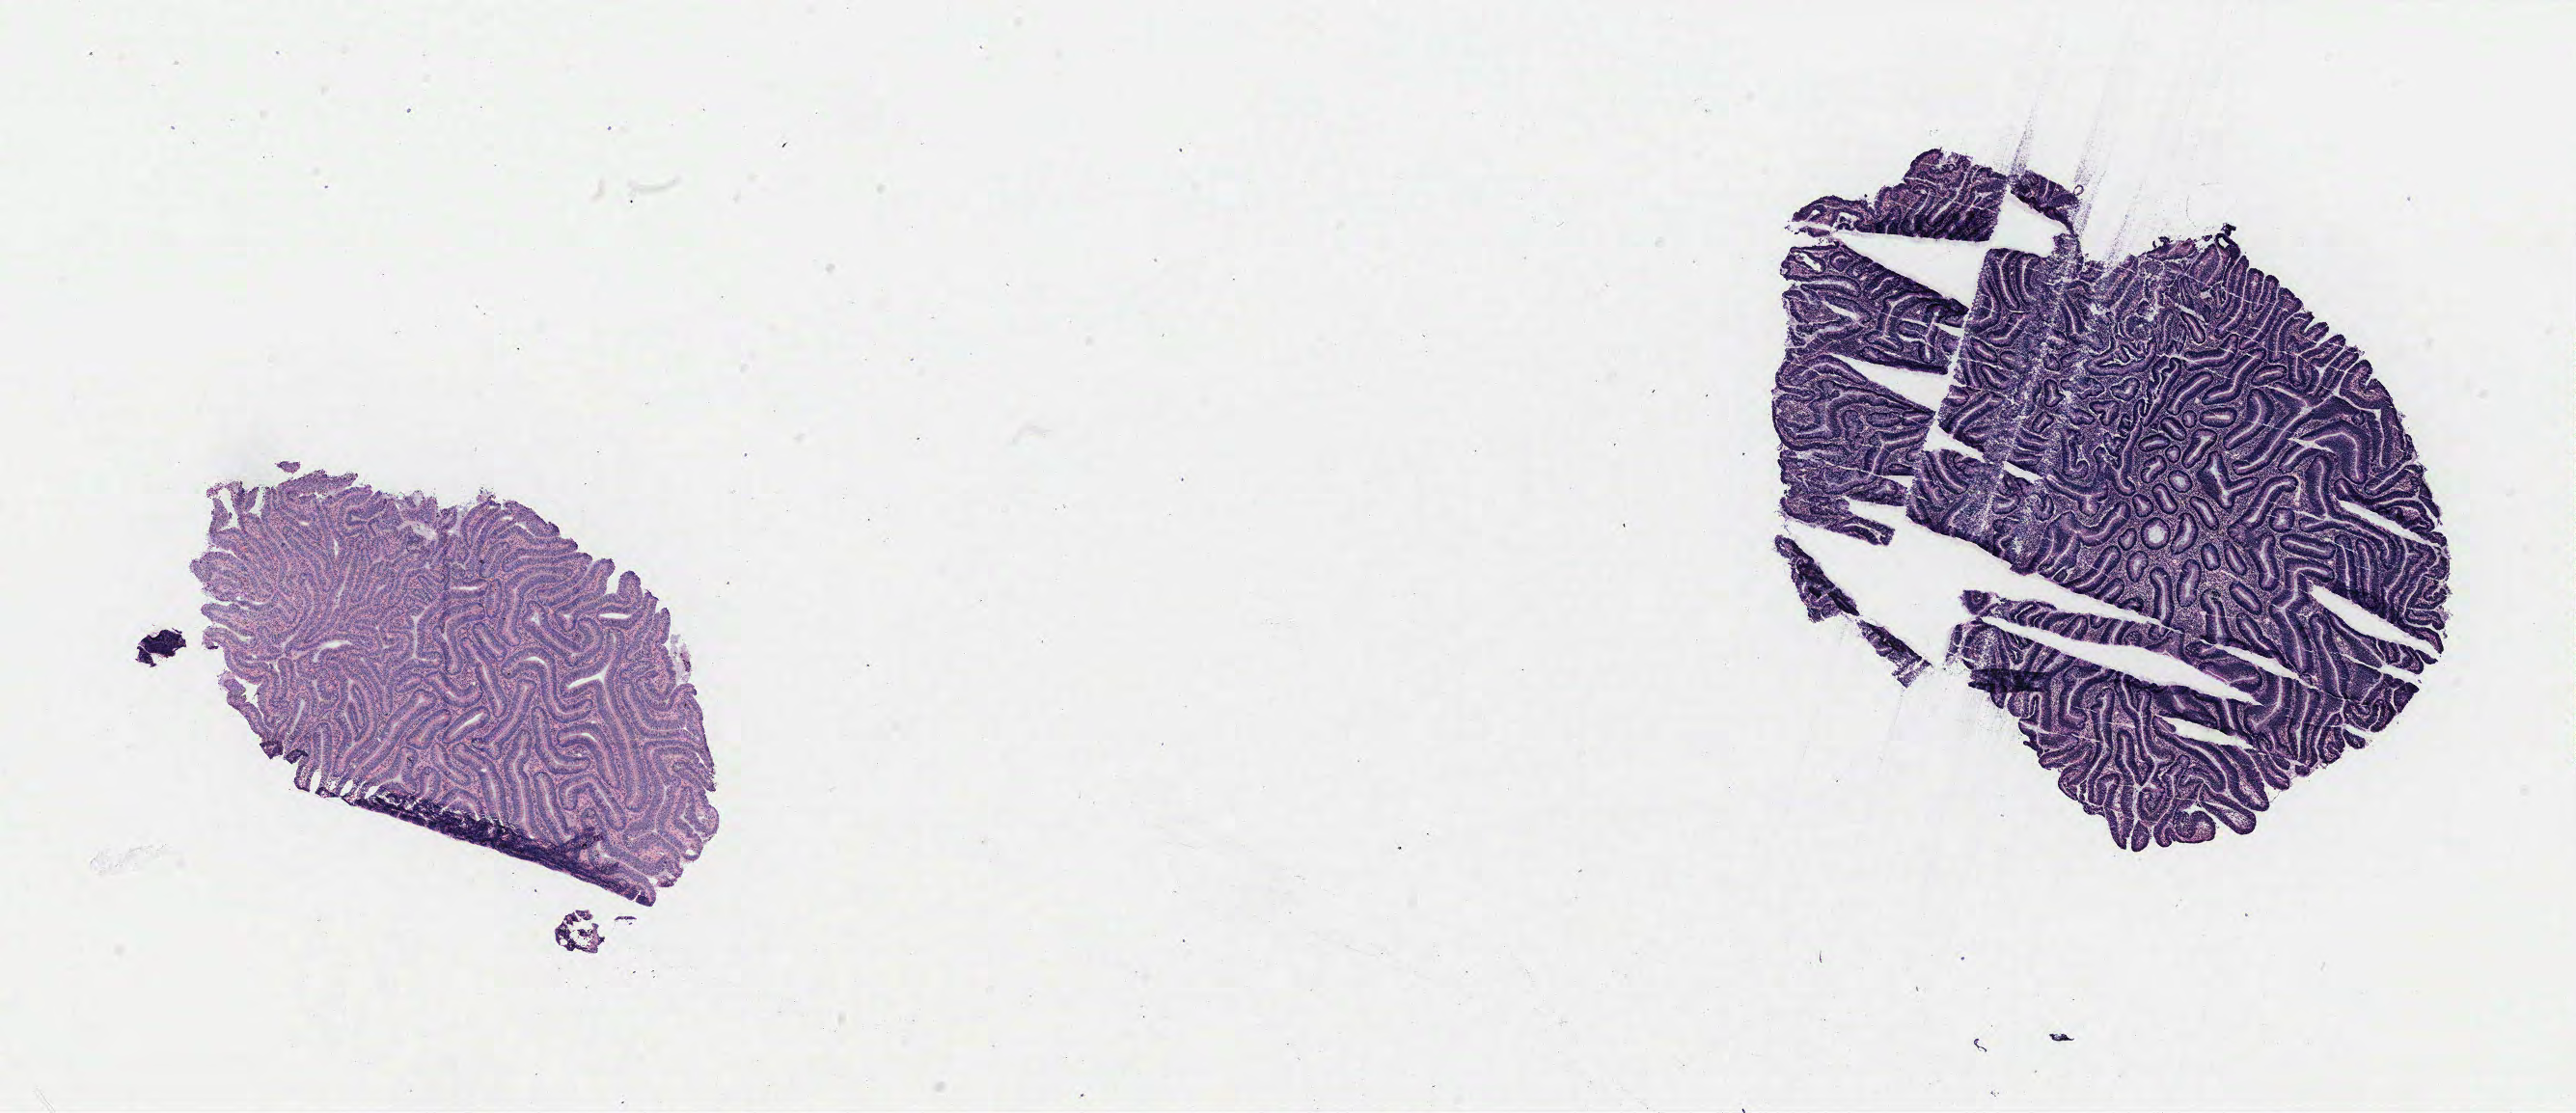
Digitized H&E-stained tissue section (whole slide) — whole scanned area (about 21.4 x 9.2 mm, acquisition: 40x scan) shown as a low-resolution overview; colon, tissue type not recorded.
Patient diagnosis (cohort enrolment): colon cancer (colon).